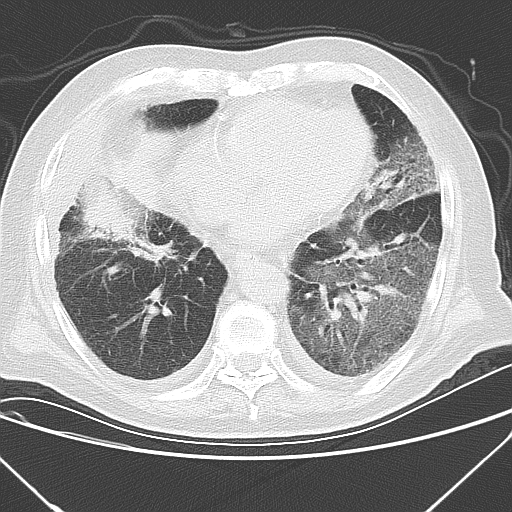
Chest CT, one axial slice; slice 10 of 43 in the series (ordered by position); lung window (W 1500 / L -600 HU); 5 mm slice thickness; 512 × 512 image matrix. Male patient, age 85 years. Case-level facts recorded for this patient, not image findings: clinical TNM (as recorded): T4 N3 M2.
Outlined on this slice (bounding box drawn by a radiologist):
- lung tumour (recorded histology: squamous cell carcinoma): bounding box [x1, y1, x2, y2] px = [122, 129, 173, 212]